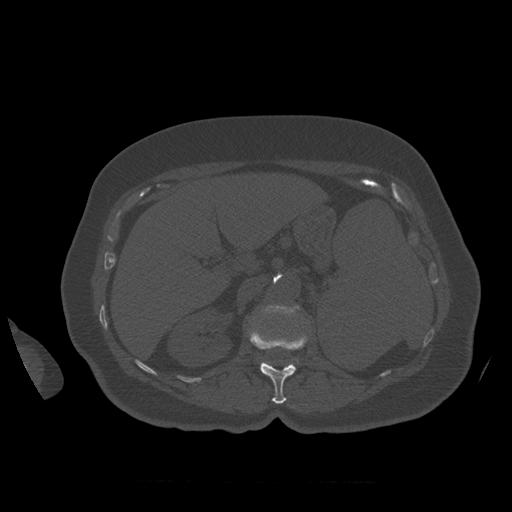
CT including the spine, one axial slice; reconstruction kernel STANDARD; 120 kVp; bone window (W 1800 / L 400 HU); 1.25 mm slice thickness; 512 × 512 image matrix, field of view 404 × 404 mm. Patient age 81 years. Case-level facts recorded for this patient, not image findings: primary cancer: renal.
Structures marked on this image (semi-automatically segmented with operator editing):
- L1 vertebra: bounding box [x1, y1, x2, y2] px = [250, 331, 307, 404]
- L2 vertebra: [265, 305, 300, 316]